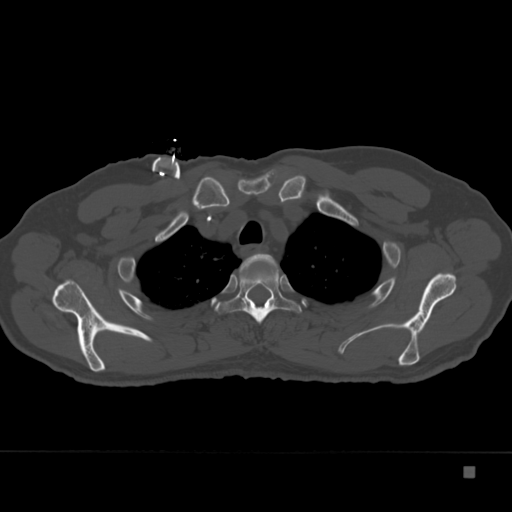
CT including the spine, one axial slice; position 289 of 332 along the scan axis; reconstruction kernel Br40s; bone window (W 1800 / L 400 HU); 1.5 mm slice thickness; 512 × 512 image matrix. Patient: male, 72 years. Case-level facts recorded for this patient, not image findings: primary cancer: skeletal.
Outlined on this slice (semi-automatically segmented with operator editing):
- T2 vertebra: bounding box <232,253,278,279> (left, top, right, bottom; pixels)
- T3 vertebra: <215,268,302,324>